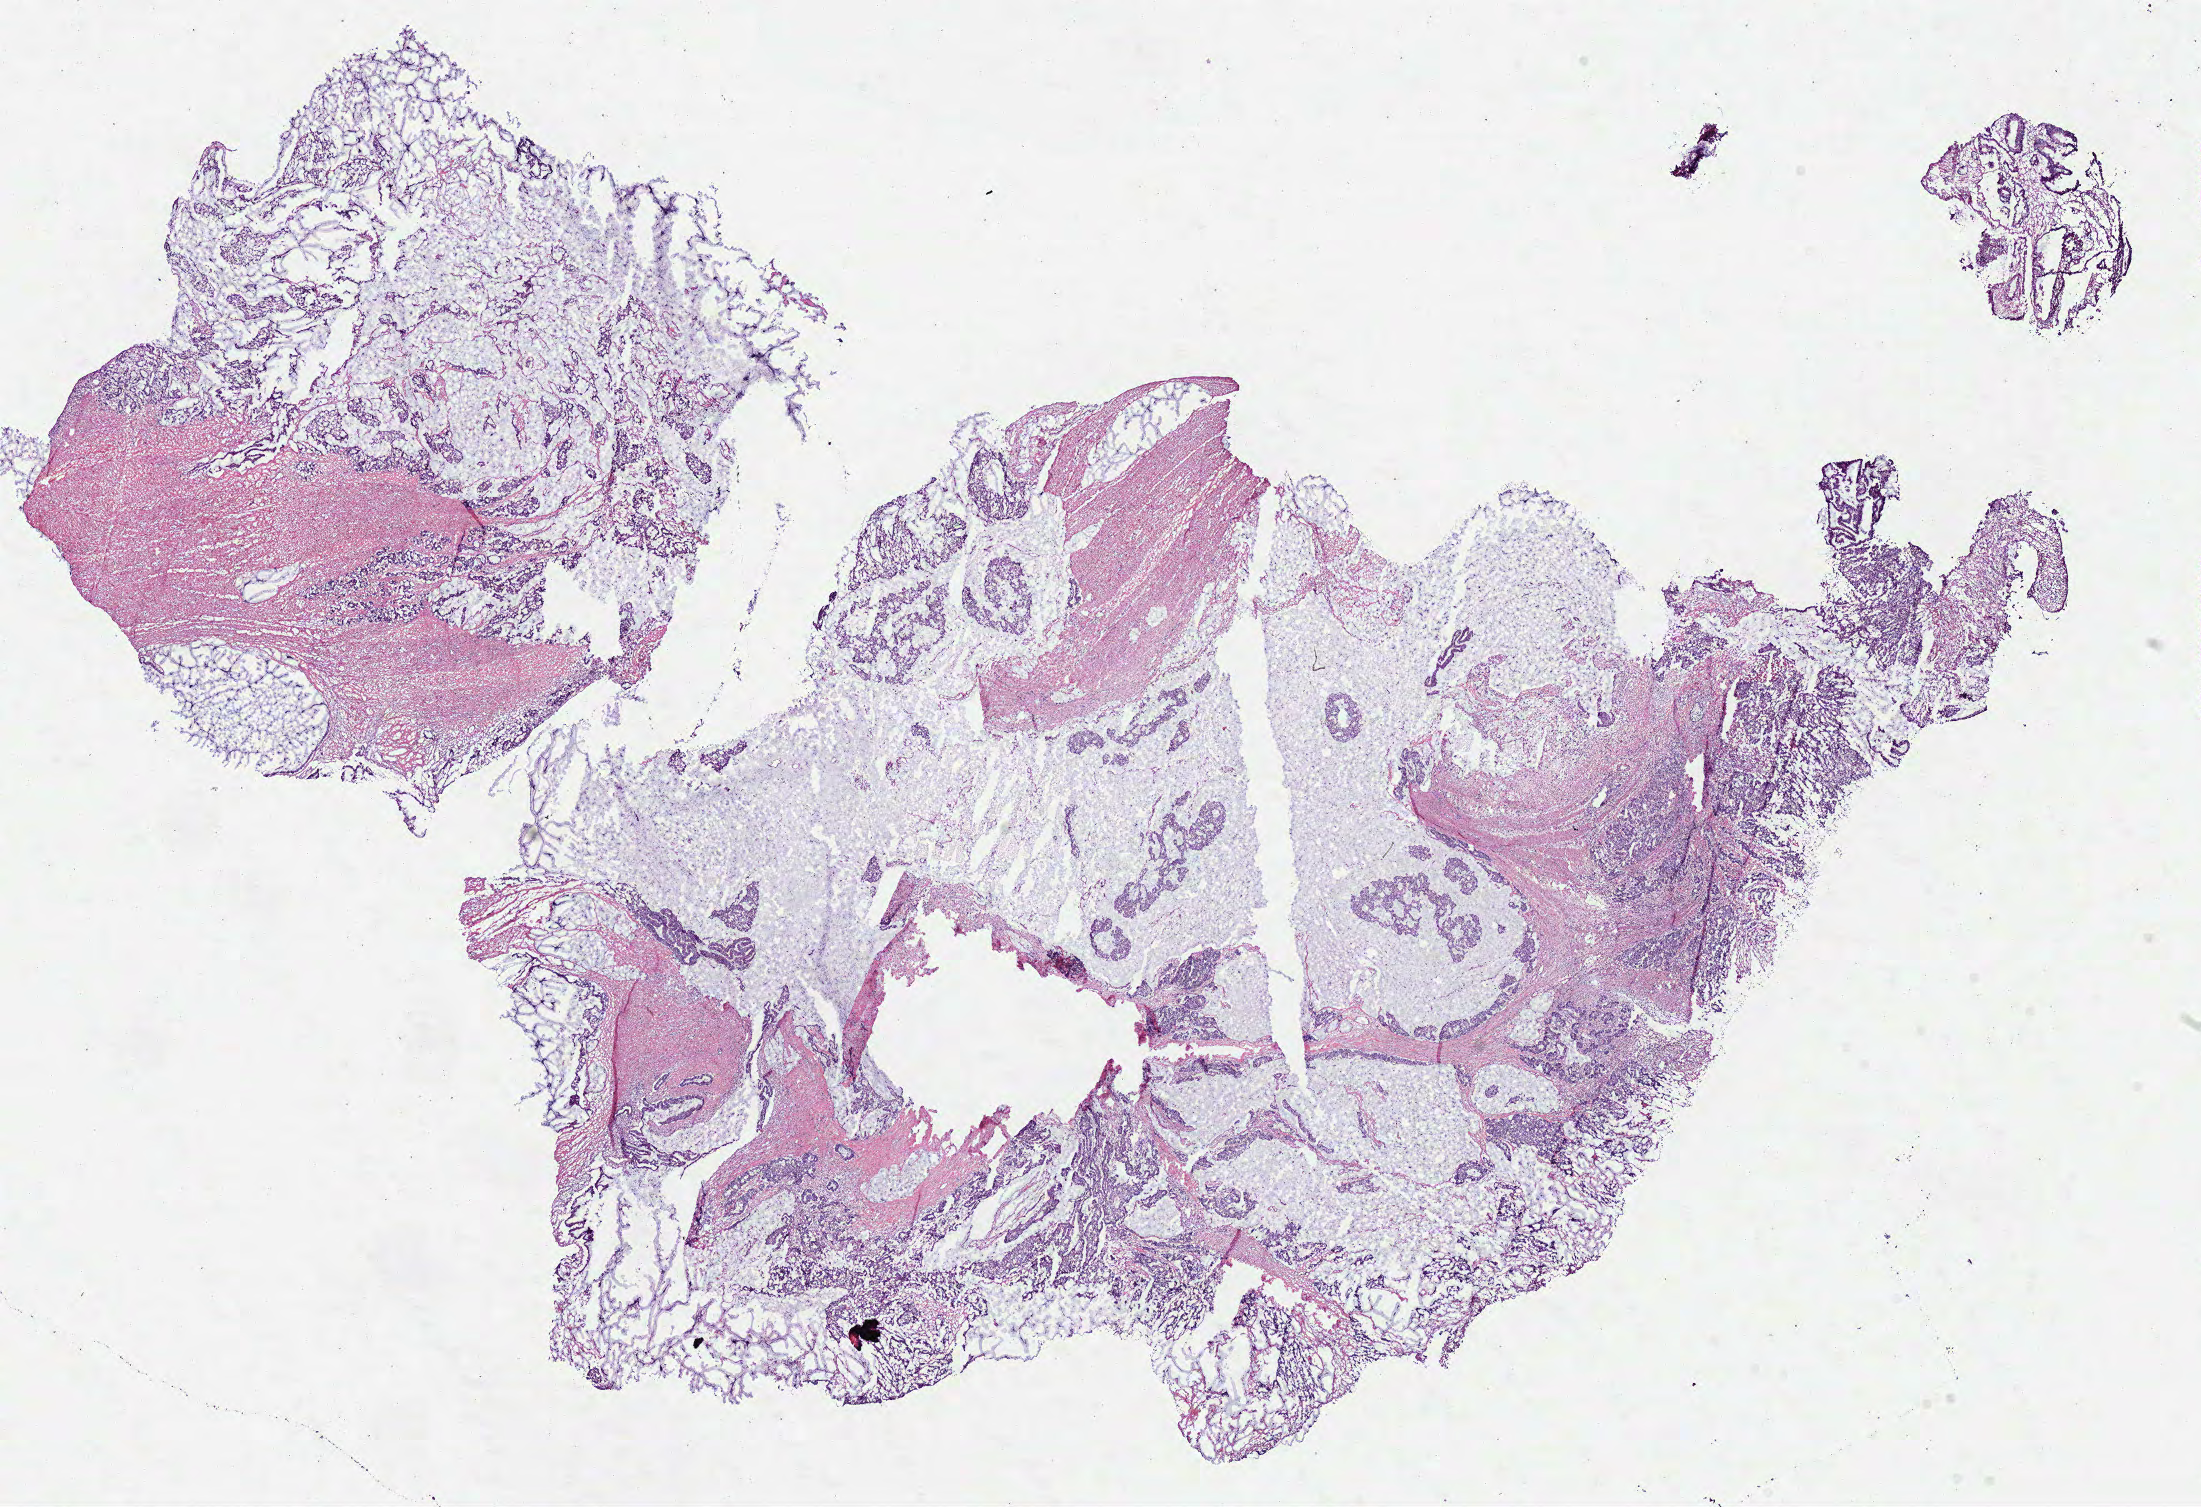
Hematoxylin and eosin (H&E) stained whole-slide image — whole scanned area (about 17.3 x 11.9 mm, slide scanned at 40x) shown as a low-resolution overview. Frozen section from the bottom of the tissue portion. Sample: primary tumour, colon. Patient: male, age at initial diagnosis 60 years. Composition of this section per pathologist review: tumour cells 82%, tumour nuclei 85%, normal cells 3%, stromal cells 15%, necrosis 0%.
AJCC pathologic stage: IIIC. Histologic diagnosis: Mucinous adenocarcinoma (sigmoid colon). Lymph nodes positive (case pathology): 13 of 18 examined.